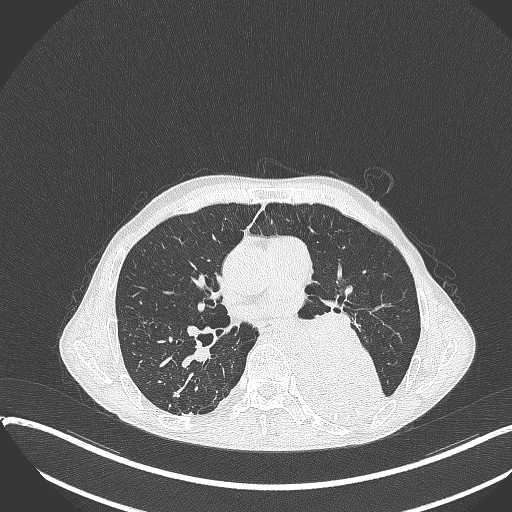
Chest CT, one axial slice. Position 195 of 401 along the scan axis. Reconstruction kernel B70f. 120 kVp. Lung window (W 1500 / L -600 HU). 1 mm slice thickness. 512 × 512 image matrix, field of view 400 × 400 mm. Male patient, age 57 years. Case-level facts recorded for this patient, not image findings: clinical TNM (as recorded): T4 N0 M0.
Annotated regions visible in this slice (rectangle marked by the reading radiologist):
- lung tumour (recorded histology: squamous cell carcinoma): box from (x=290, y=331) to (x=388, y=425) px